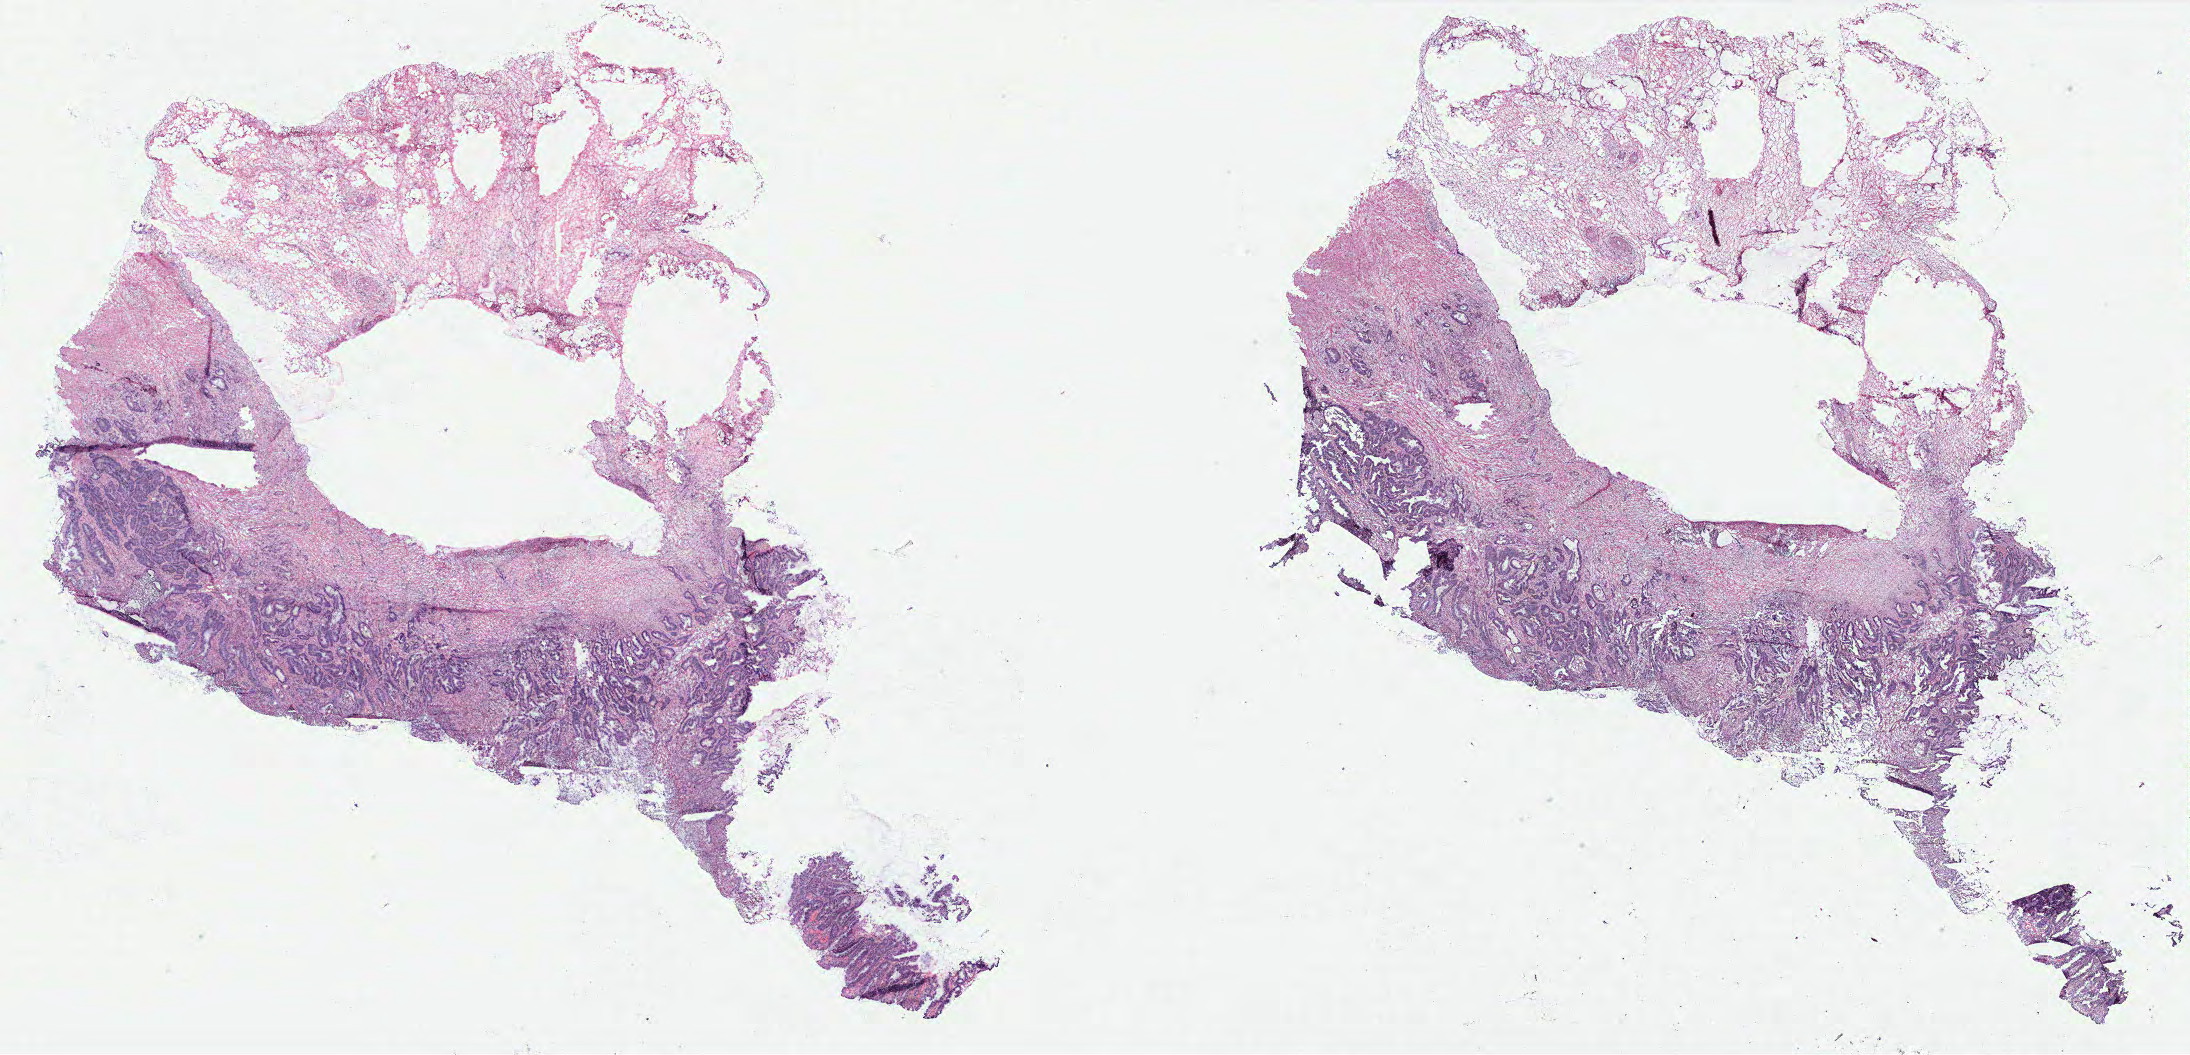
Hematoxylin and eosin (H&E) stained whole-slide image, a low-resolution overview of the entire scanned area, about 35.1 x 16.9 mm, colon, tissue type not recorded.
• patient diagnosis (cohort enrolment): colon cancer (colon)